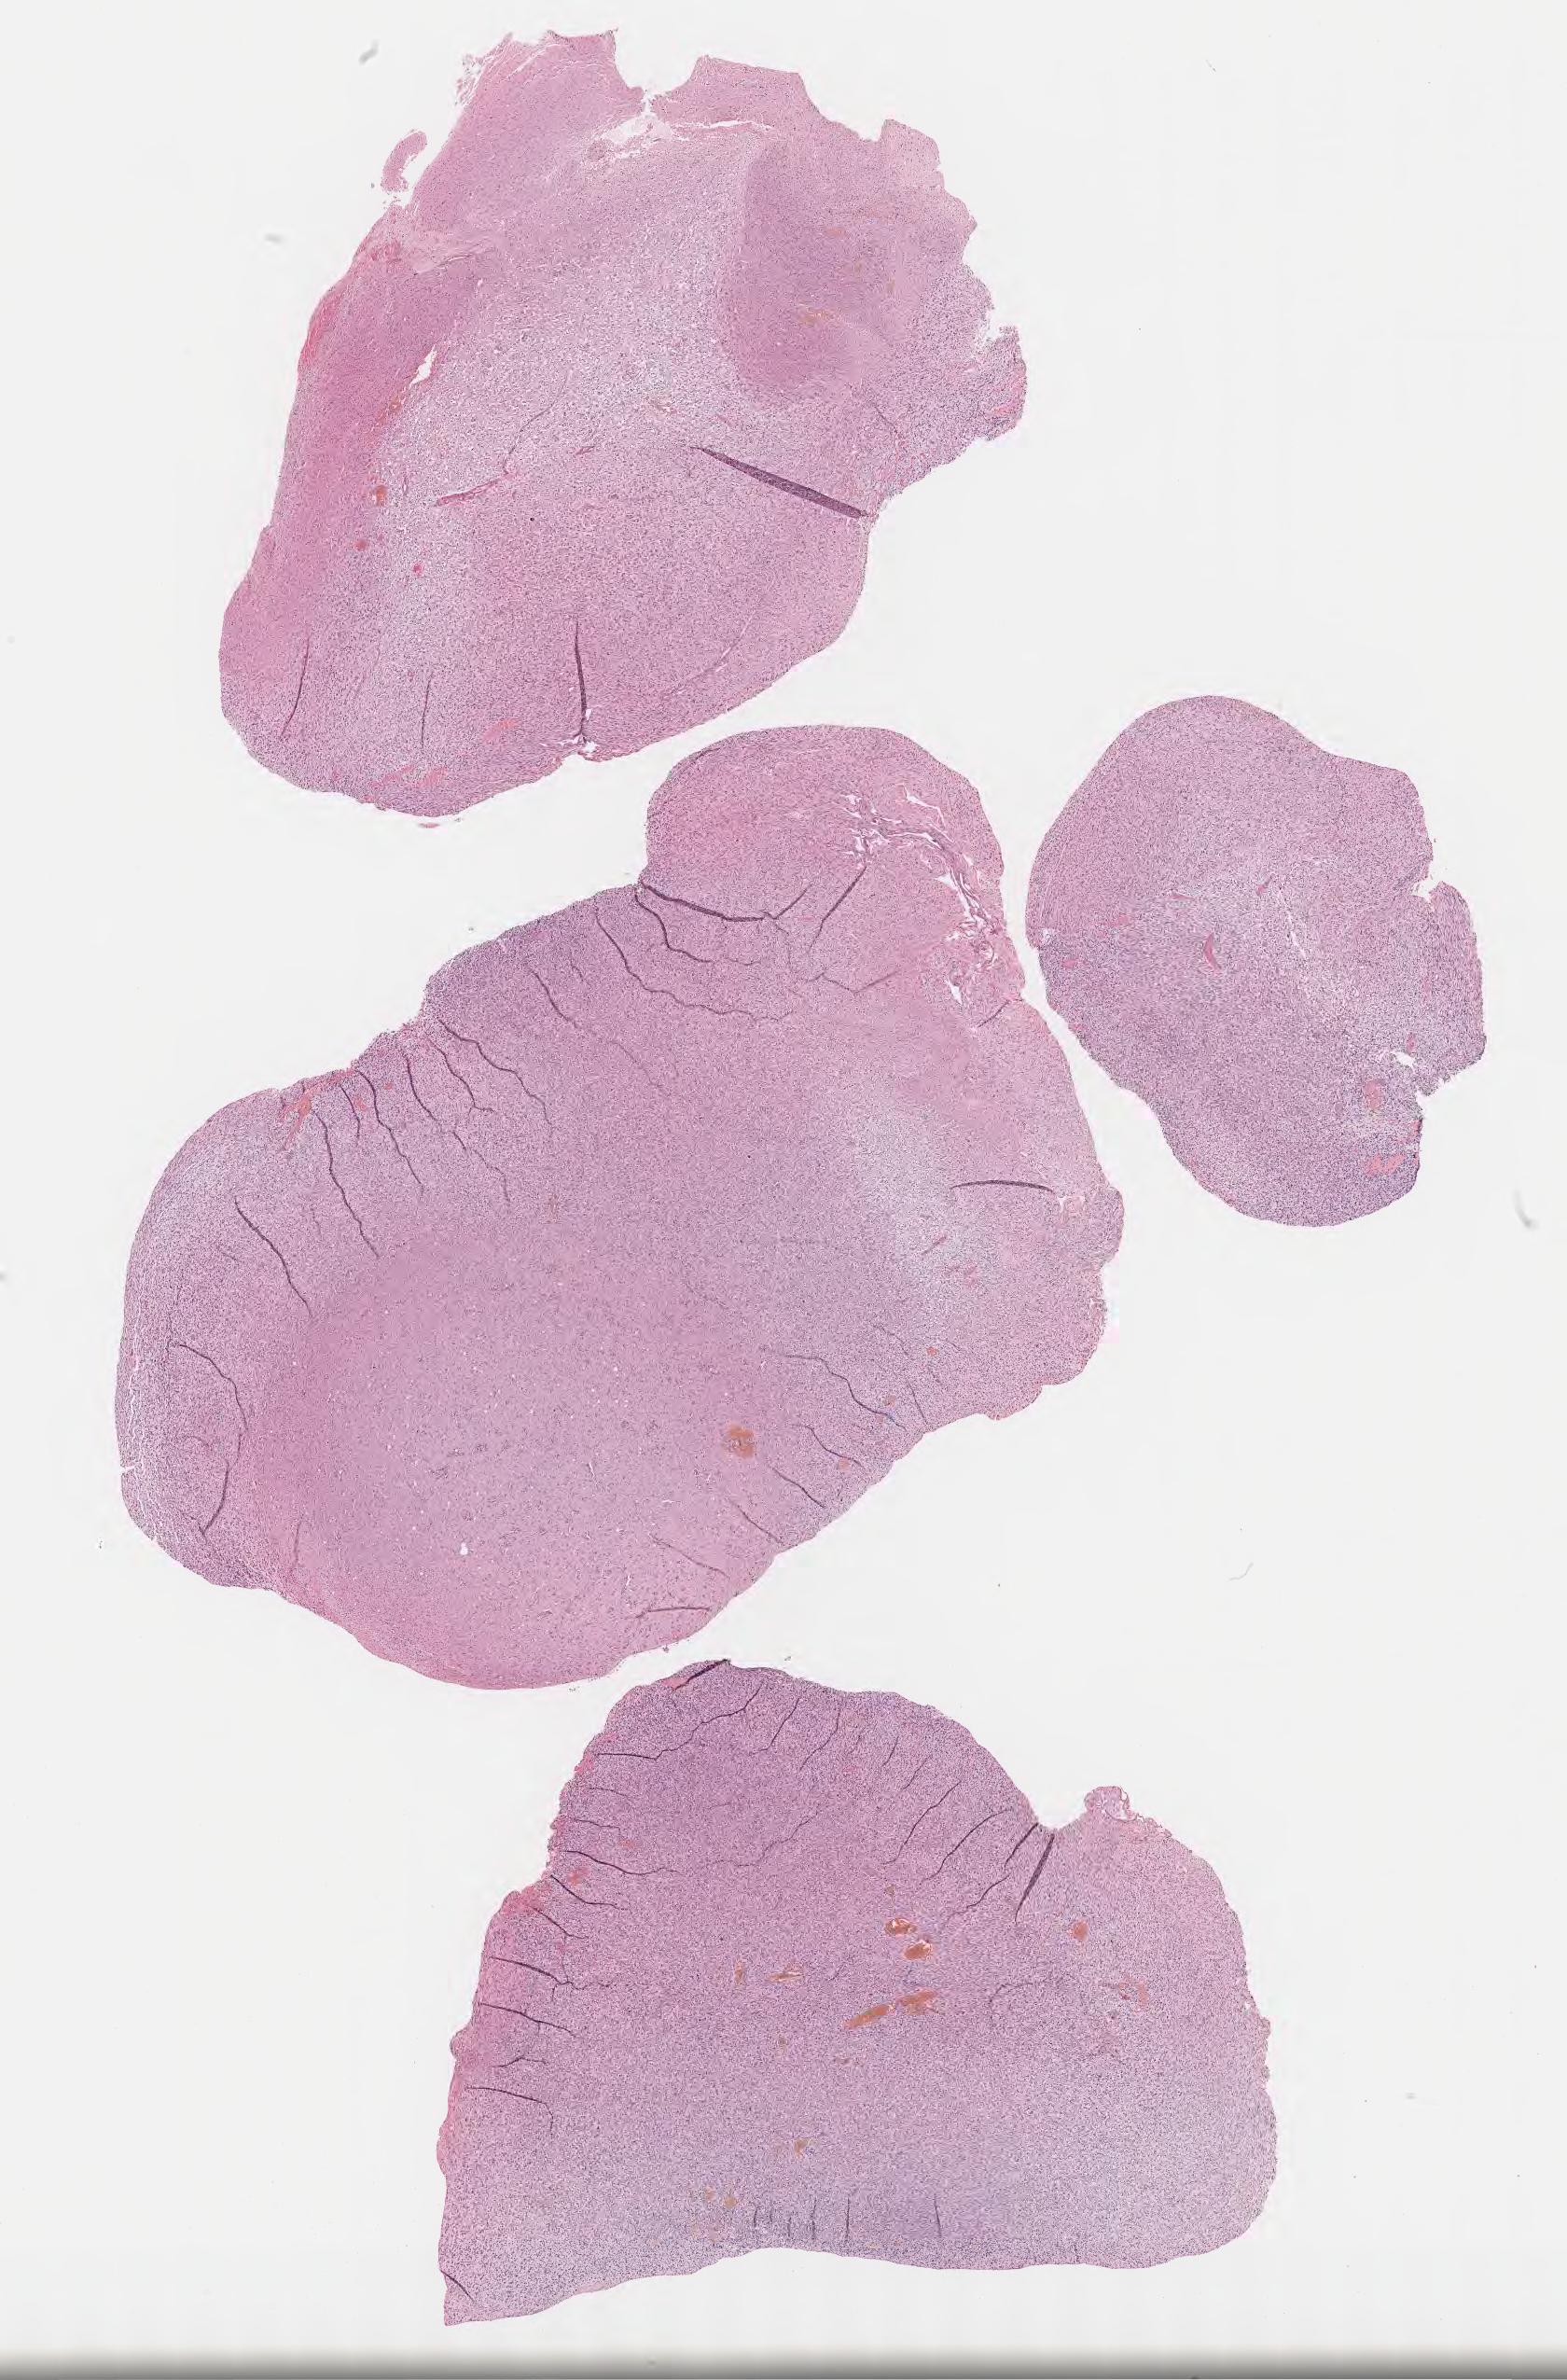
Digitized H&E-stained section — whole scanned area (about 13.6 x 20.6 mm) shown as a low-resolution overview, formalin-fixed paraffin-embedded section, primary tumor, anatomic site: brain. Male, age 66 years at initial diagnosis.
Diagnosis: Glioblastoma, NOS.